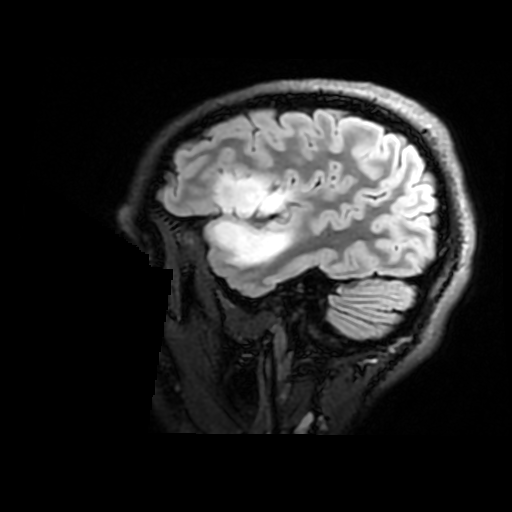
Brain MRI from a brain-tumour surgery series, one sagittal slice; slice 135 of 176 in the series (ordered by position); T2 FLAIR; 1 mm slice thickness; 512 × 512 image matrix, field of view 240 × 240 mm. Case-level facts recorded for this patient, not image findings: histopathology: Astrocytoma; WHO grade: 2; IDH mutation: yes; tumour location: Right Insular.
Annotated regions visible in this slice (manually delineated by an expert):
- tumour: bounding box <213,176,299,267> (left, top, right, bottom; pixels)